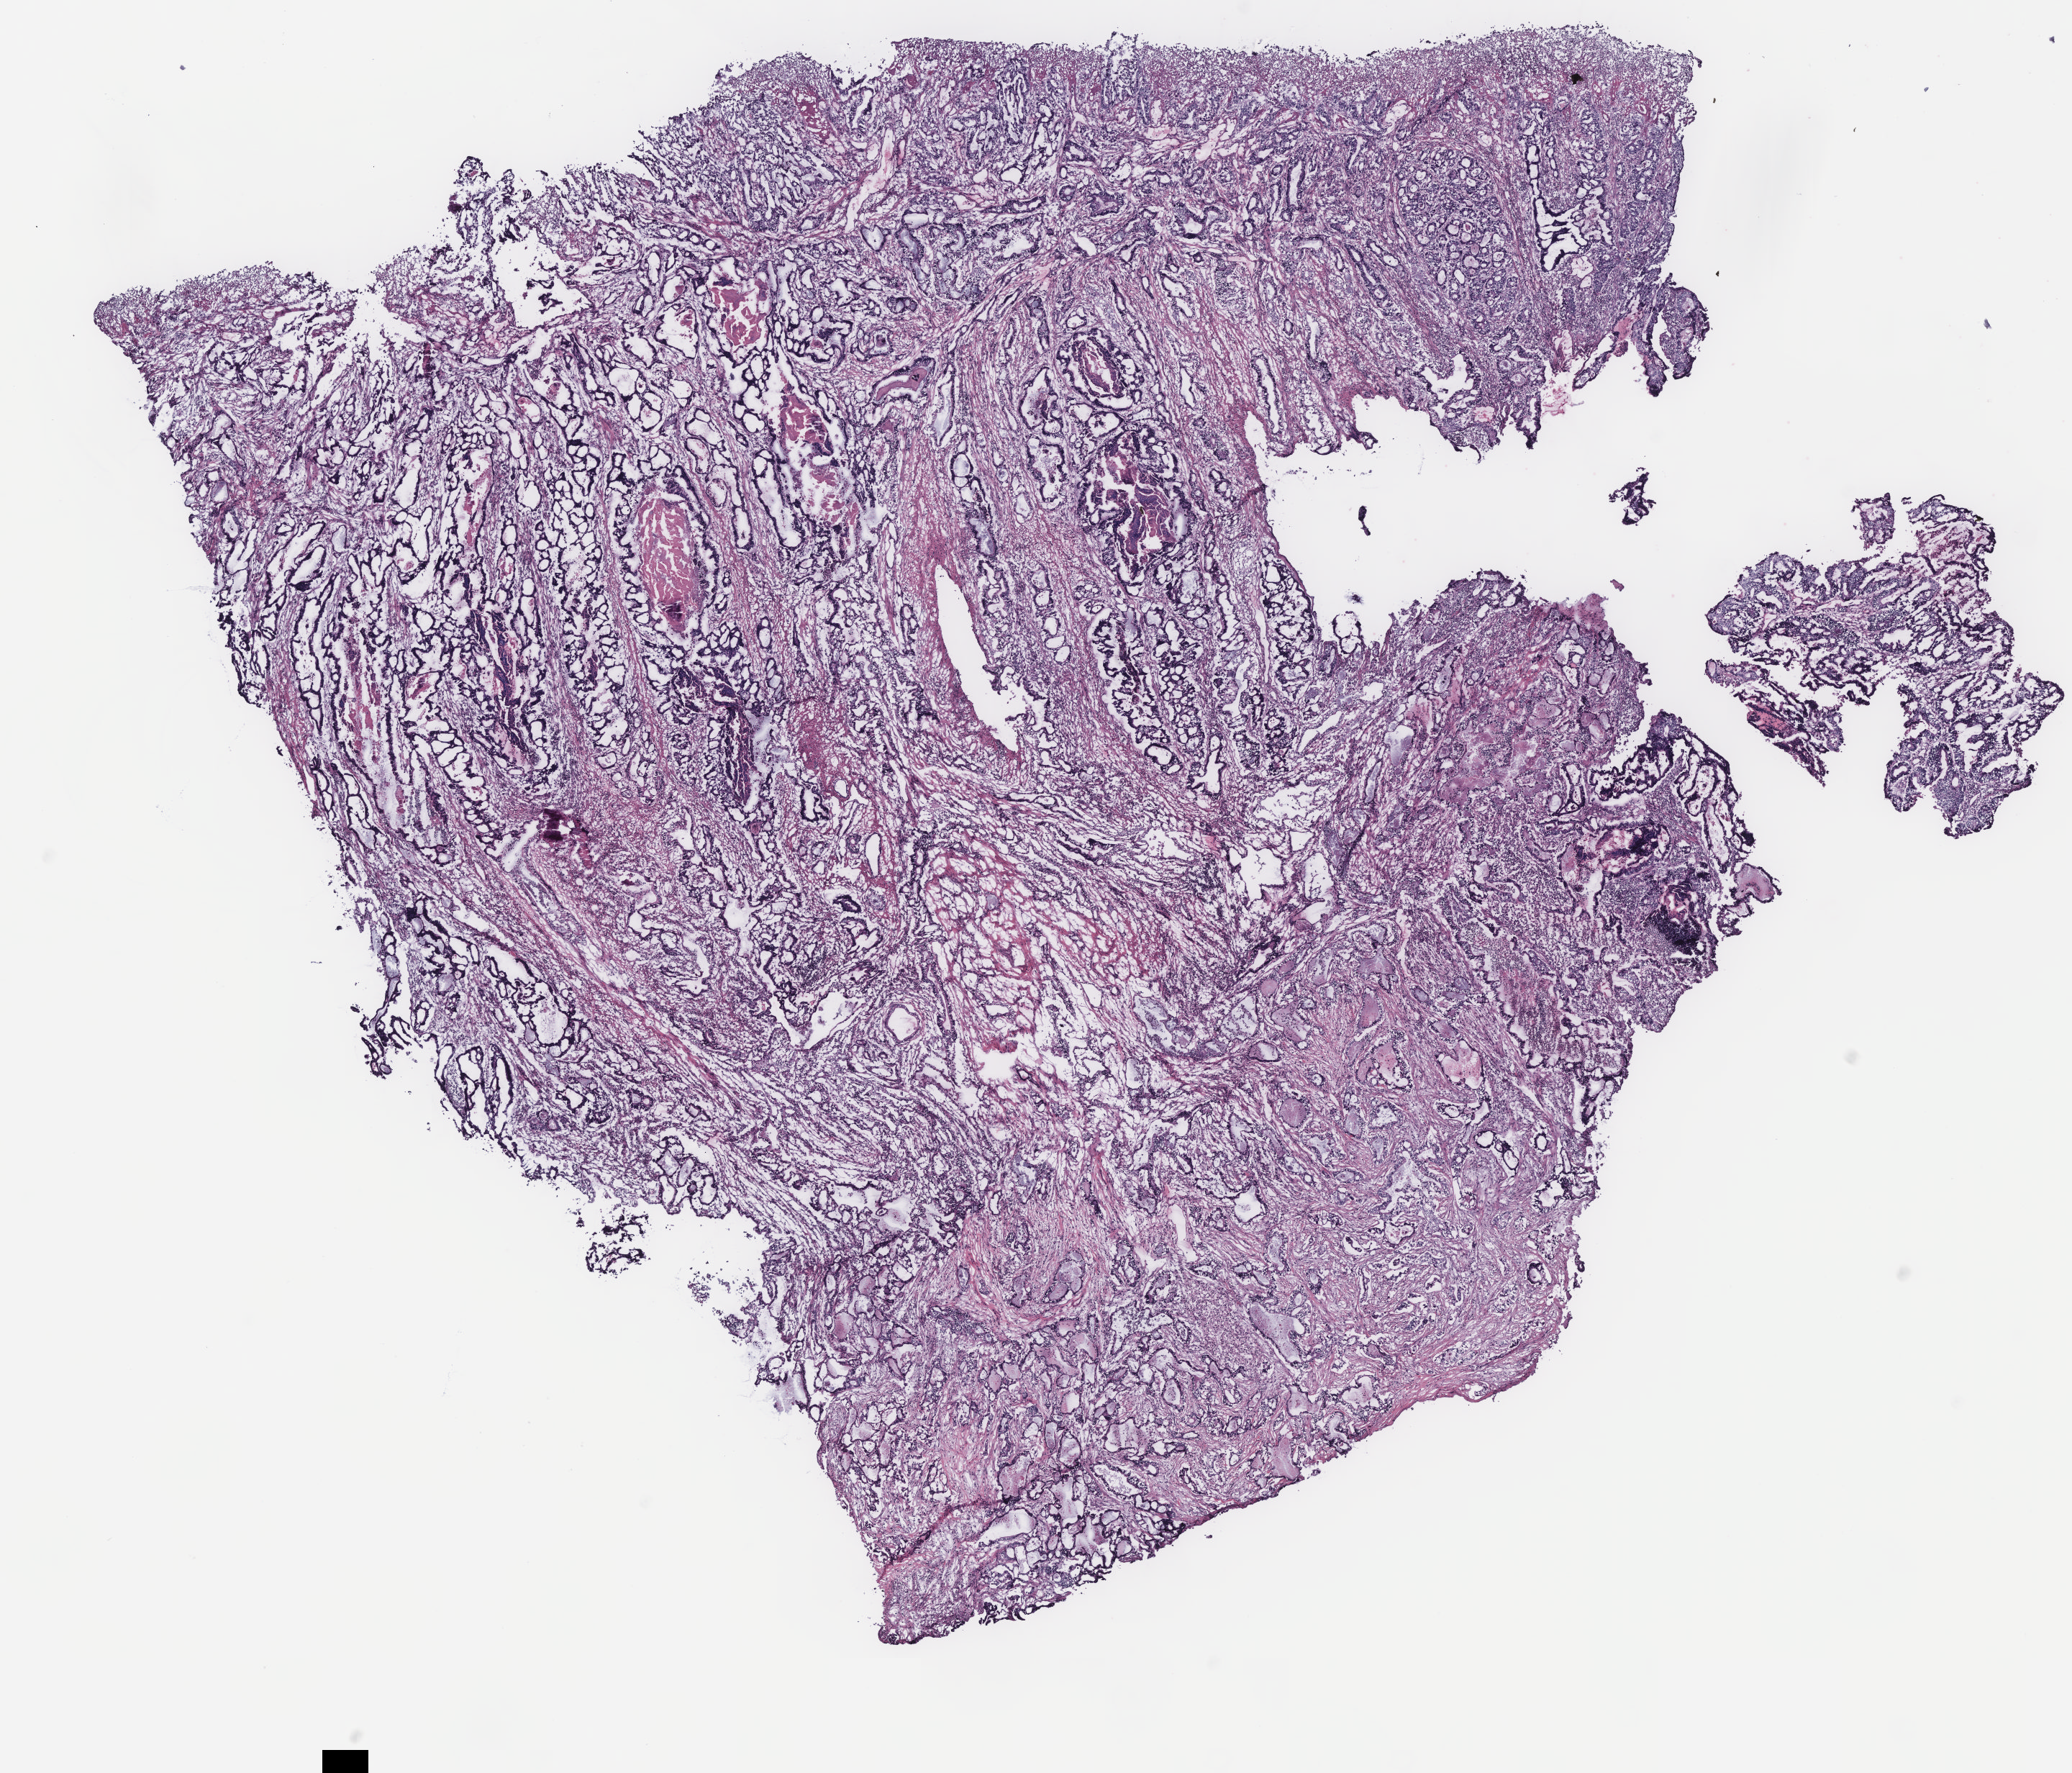
Digitized H&E-stained tissue section (whole slide), whole scanned area (about 11.5 x 9.9 mm) shown as a low-resolution overview. Colon, tissue type not recorded. Female patient.
* patient diagnosis: Adenocarcinoma, NOS